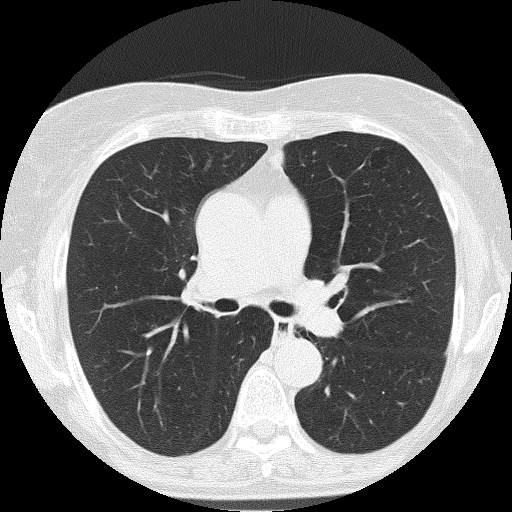
Low-dose screening chest CT, one axial slice; position 106 of 166 along the scan axis; reconstruction kernel FC51; 120 kVp; lung window (W 1500 / L -600 HU); 2 mm slice thickness; 512 × 512 image matrix.
Outlined on this slice (outlined manually by an expert reader):
- lesion 2 (nodule, upper lobe of left lung): bounding box <275,153,283,168> (left, top, right, bottom; pixels)